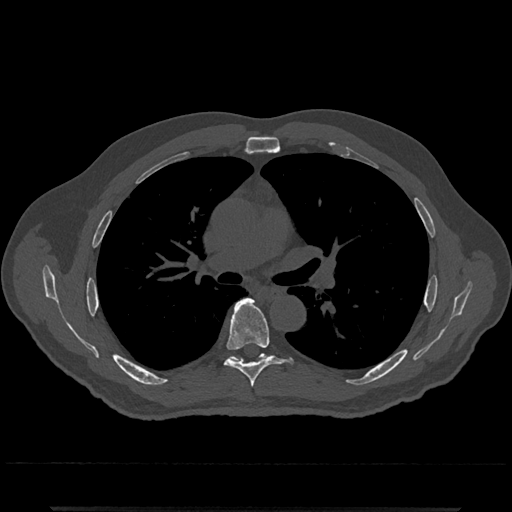
CT including the spine, one axial slice. Position 769 of 797 along the scan axis. Reconstruction kernel Br40s/3. Bone window (W 1800 / L 400 HU). 0.5 mm slice thickness. 512 × 512 image matrix, field of view 393 × 393 mm. Patient: male, 67 years. Case-level facts recorded for this patient, not image findings: primary cancer: prostate.
Annotated regions visible in this slice (semi-automatically segmented with operator editing):
- T6 vertebra: bounding box (x1, y1, x2, y2) in pixels: (224, 298, 280, 387)
- T7 vertebra: (230, 354, 267, 358)